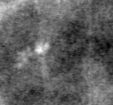
Cropped region of a digitized screen-film mammogram centred on a radiologist-marked abnormality; left breast; MLO view; BI-RADS breast density category 4 (scale 1–4).
Calcifications, morphology pleomorphic, distribution clustered; BI-RADS assessment category 4; subtlety rating 2 on a 1 (subtle) to 5 (obvious) scale; pathology (as recorded): benign.